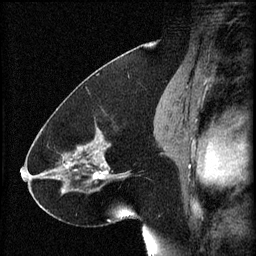
Breast MRI (dynamic contrast-enhanced), one sagittal slice. Position 34 of 60 along the scan axis. 3 images stored at this slice position (order not interpretable as contrast timing). 1.5 T. TE 4.2 ms, TR 8.2 ms. 2 mm slice thickness. 256 × 256 image matrix, field of view 180 × 180 mm. Patient: female, 41 years.
Outlined on this slice (semi-automatically segmented with operator editing):
- analysis volume of interest (the breast-tissue region the enhancement analysis was run in; not a lesion): box from (x=72, y=120) to (x=134, y=195) px
- tumour enhancement mask (voxels above the 70 % enhancement threshold inside the analysis volume of interest): (x=72, y=128)–(x=130, y=181)